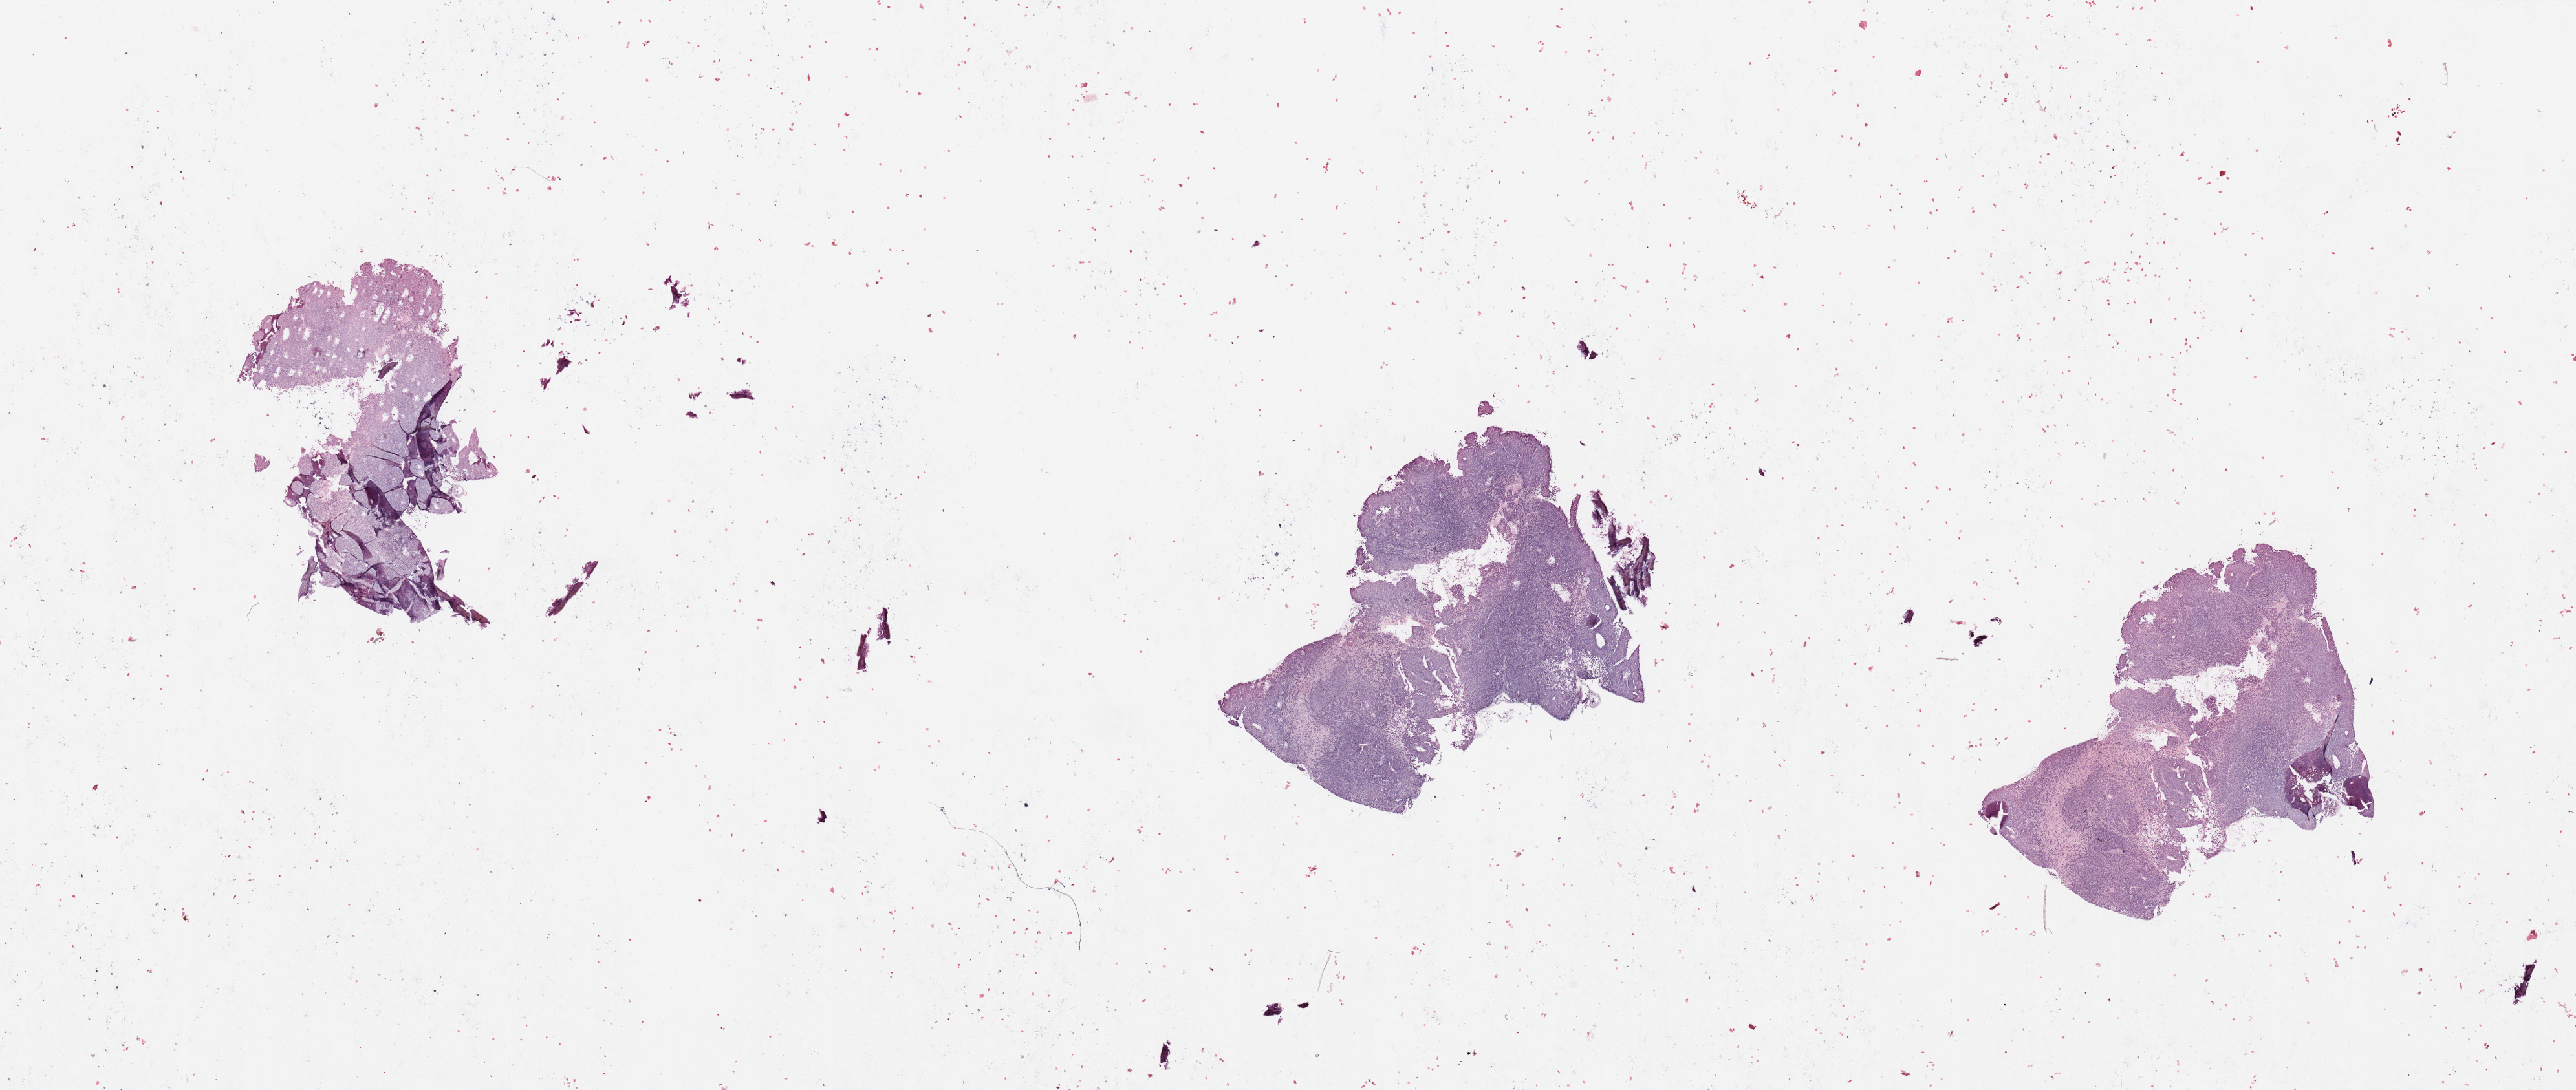
Digitized H&E-stained tissue section (whole slide), low-resolution overview of the scanned area, about 31.5 x 13.3 mm (acquisition: 20x scan); tumour tissue sample, sampled site: lymph node. Female, 55 y/o. Slide review estimates, as recorded: tumour nuclei 90%, necrosis 0%.
- this section: metastatic tumour tissue
- patient diagnosis: Malignant melanoma, NOS